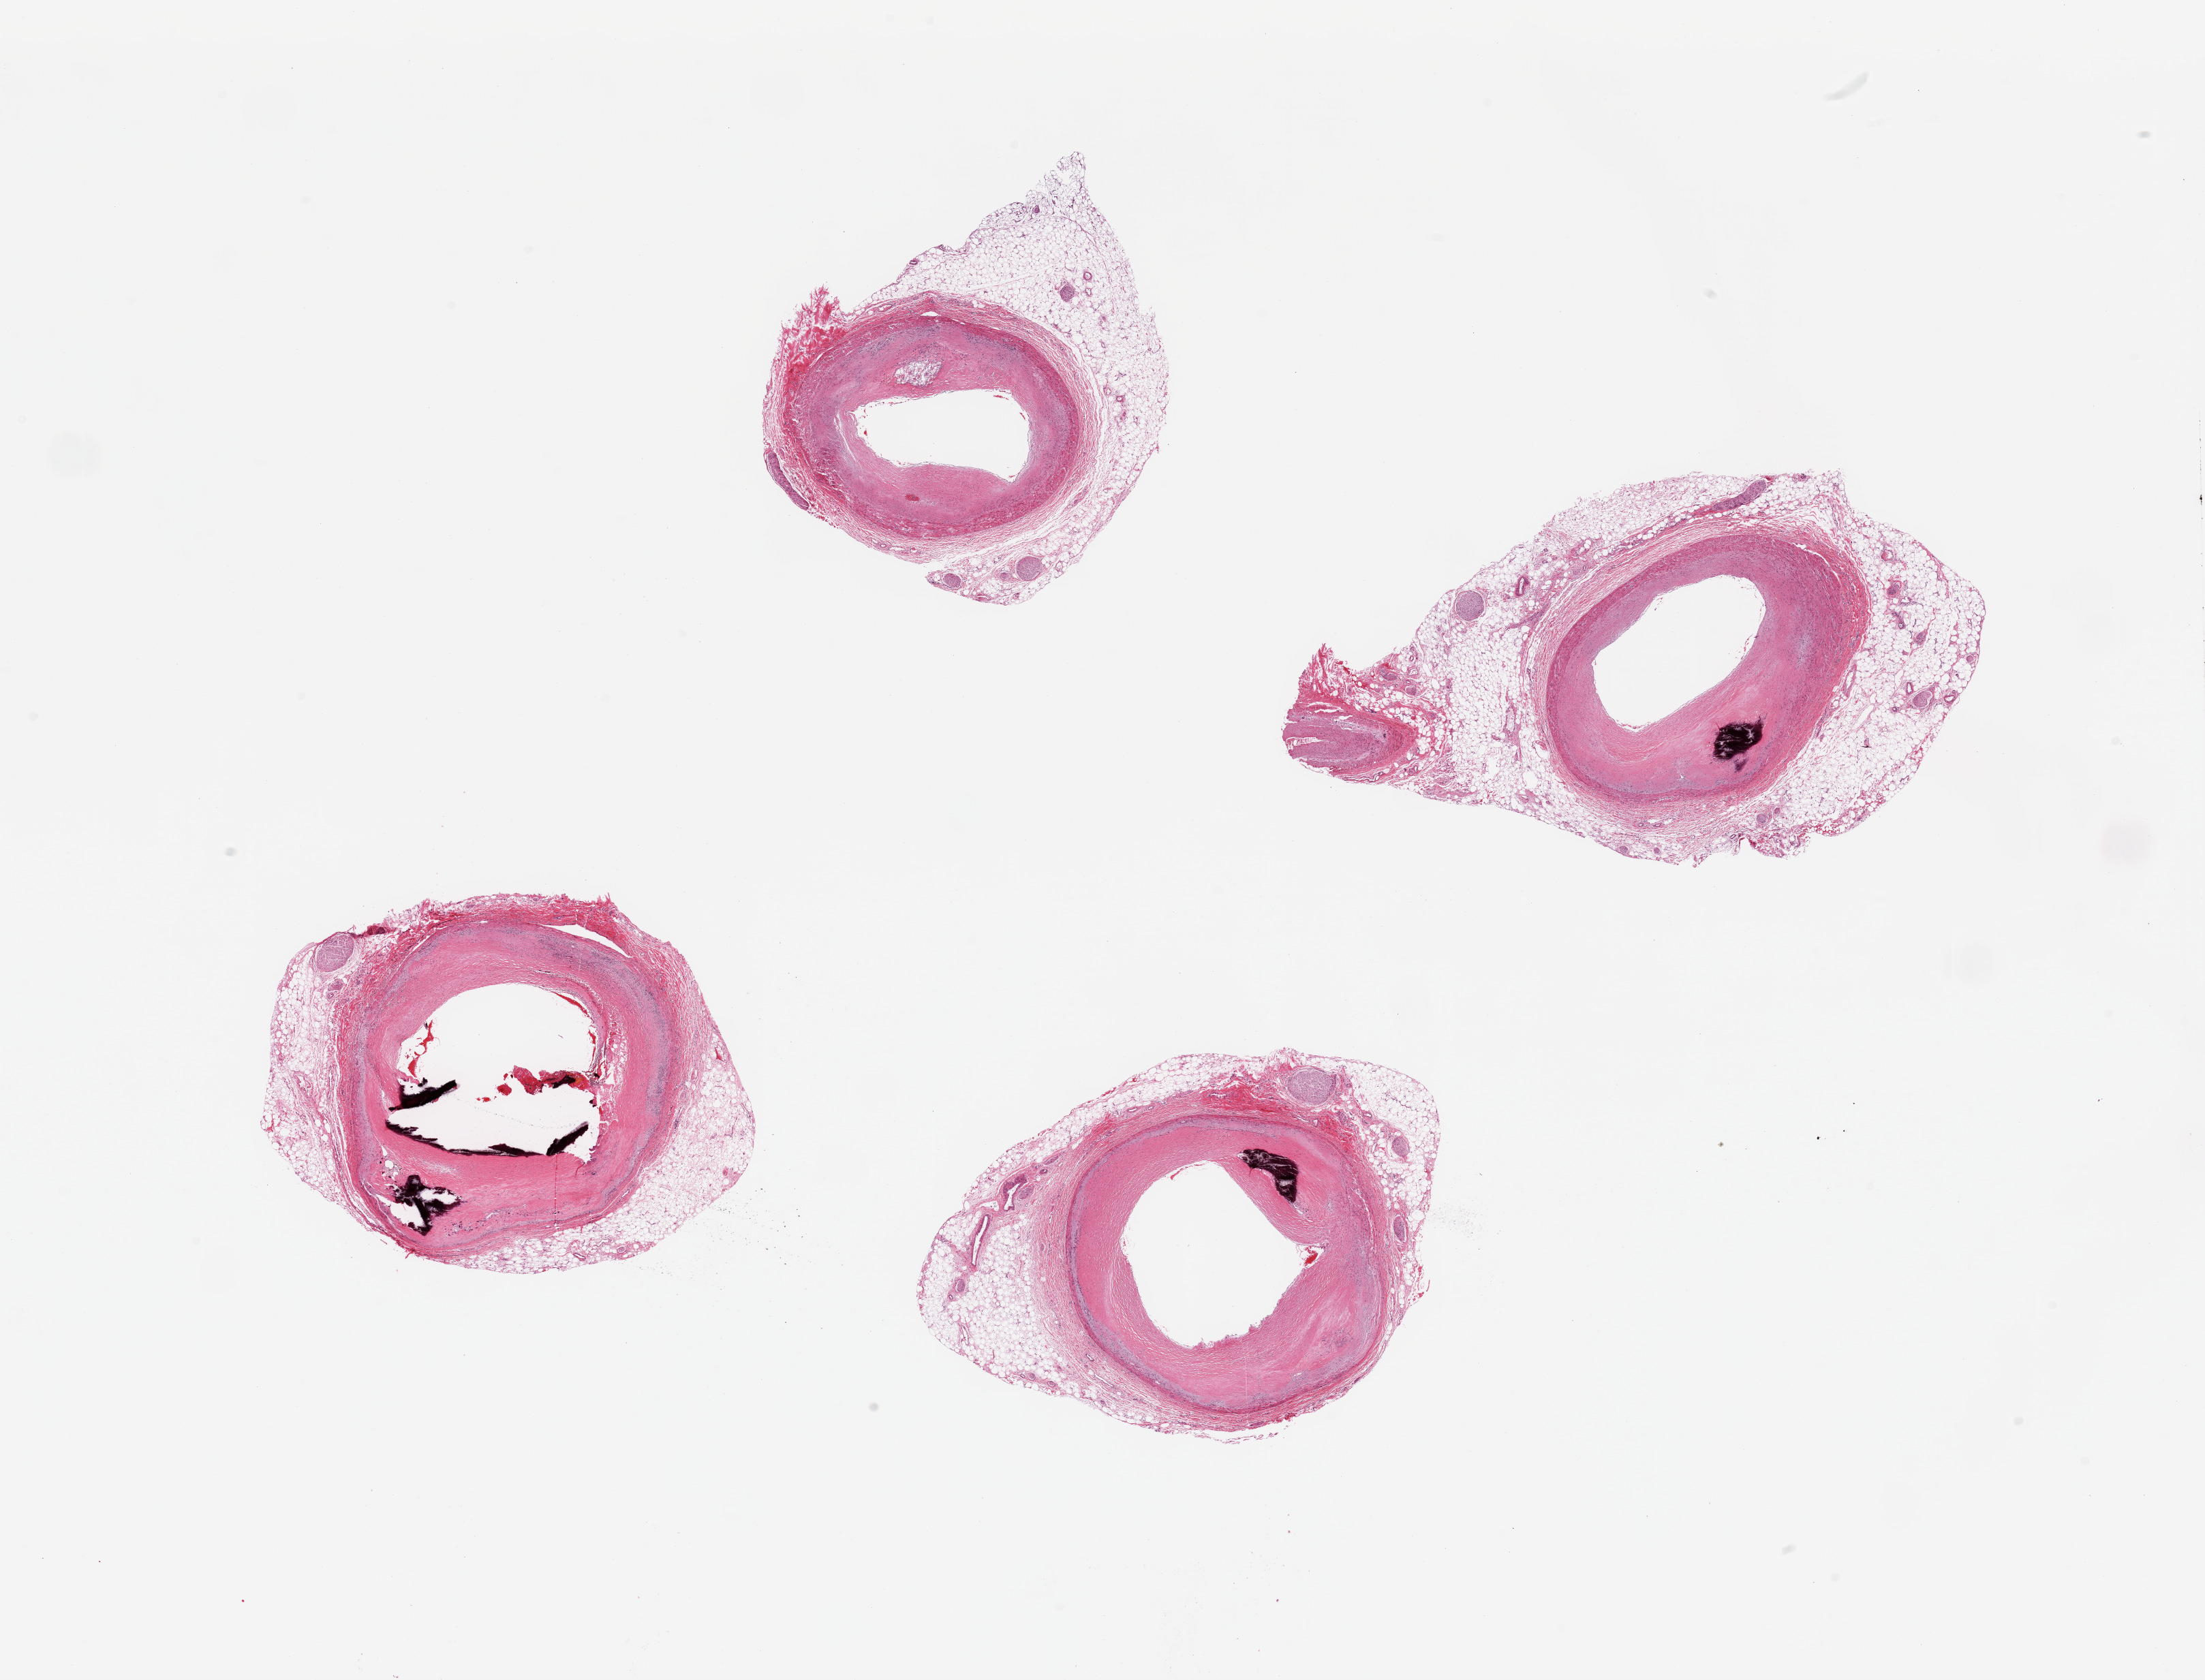
Digitized haematoxylin and eosin-stained section, a low-resolution overview of the entire scanned area, about 25.6 x 19.5 mm (acquisition: 20x scan). PAXgene-fixed, paraffin-embedded tissue. Sampled site (target tissue): coronary artery. Tissue donor sample. Male donor.
- review note (as recorded): 4 pieces; extensive replacement of intima & media by fibrous & atheromatous, focally calcified, material, but lumen patent; up to 1.6mm perivascular intrimmed fat